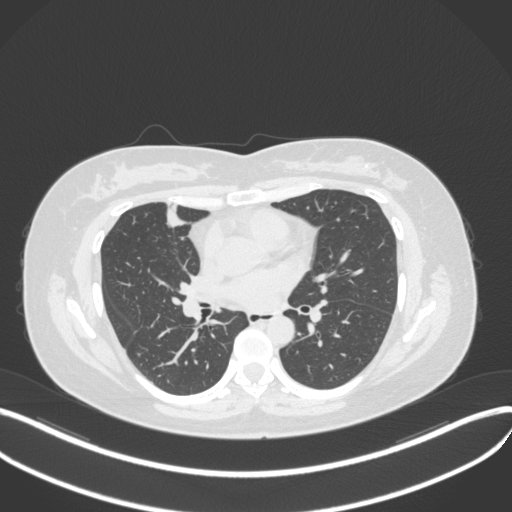
Chest CT, one axial slice; position 162 of 272 along the scan axis; lung window (W 1500 / L -600 HU); 1 mm slice thickness; 512 × 512 image matrix. Patient: female, 42 years. Case-level facts recorded for this patient, not image findings: clinical TNM (as recorded): T1b N0 M0.
Structures marked on this image (rectangle marked by the reading radiologist):
- lung tumour (recorded histology: adenocarcinoma): bounding box (x1, y1, x2, y2) in pixels: (162, 200, 187, 230)